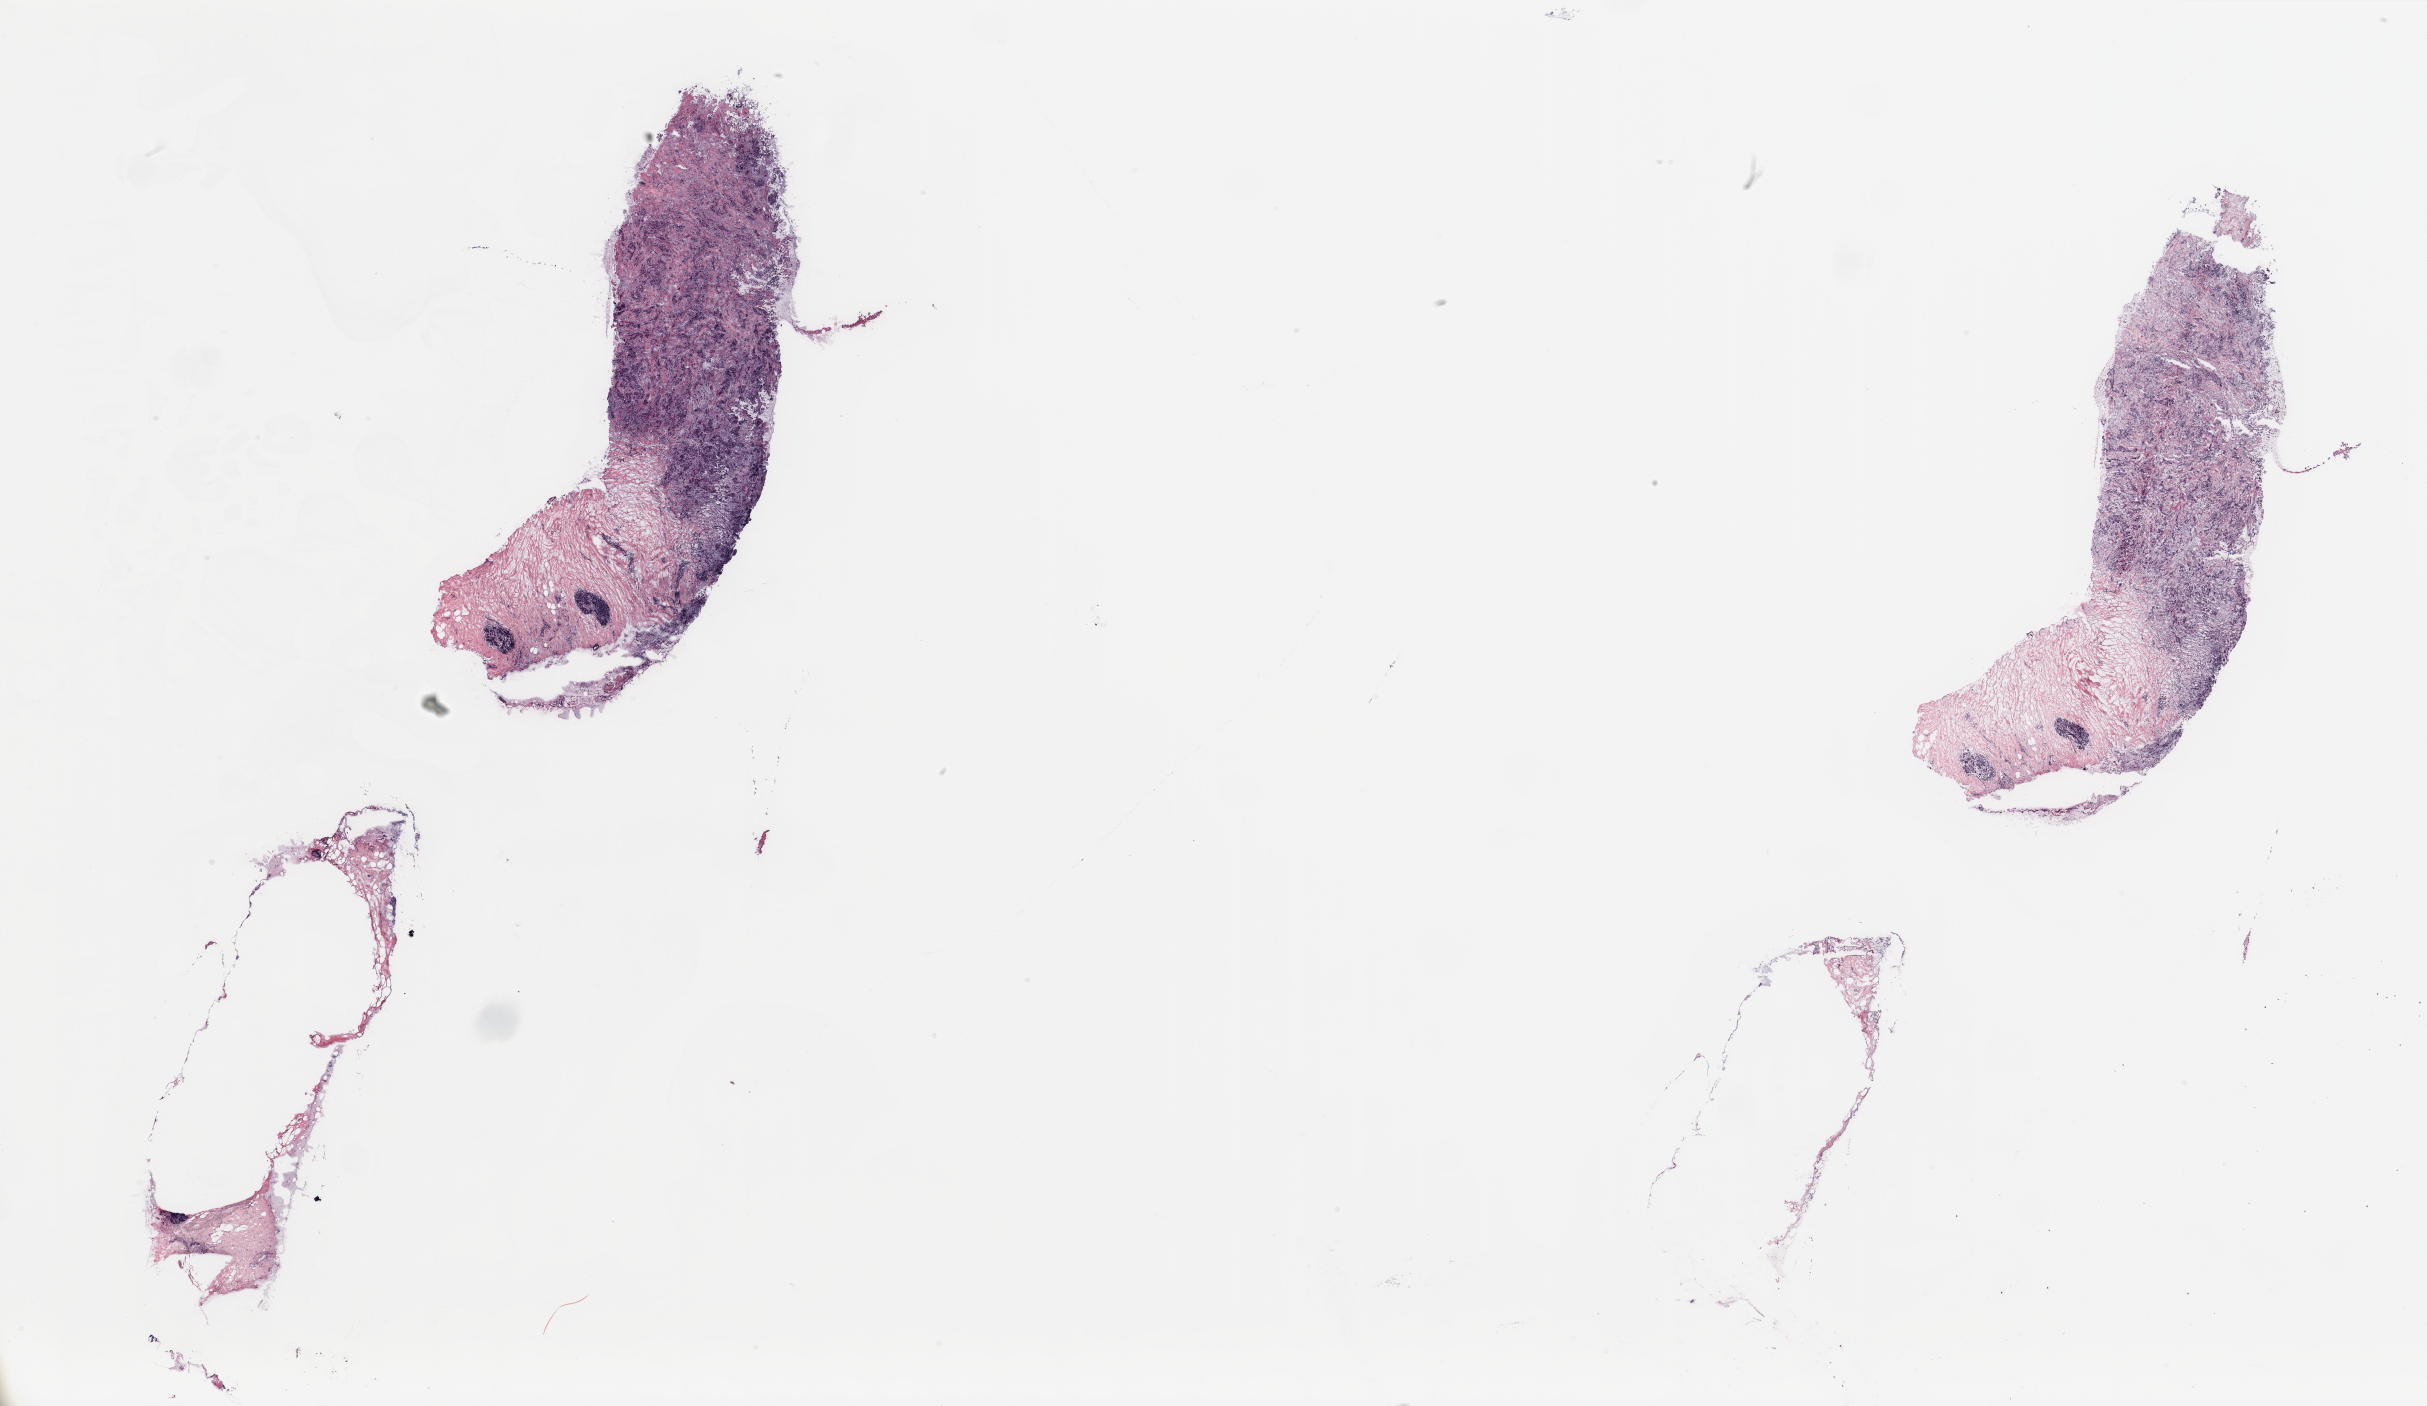
H&E whole-slide image, a low-resolution overview of the entire scanned area, about 38.4 x 22.2 mm (acquisition: 20x scan); breast, tissue type not recorded.
* patient diagnosis (cohort enrolment): breast cancer (breast)